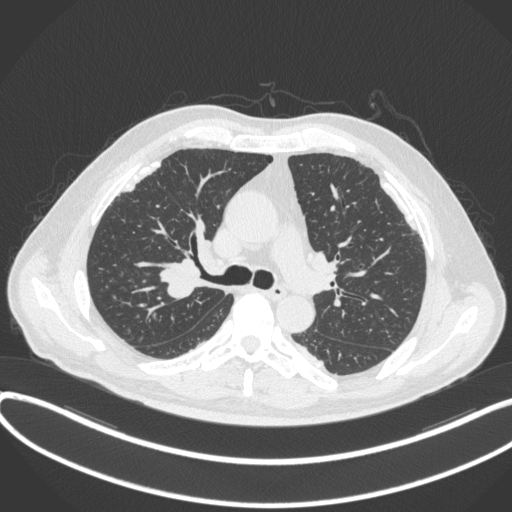
Chest CT, one axial slice; position 274 of 455 along the scan axis; reconstruction kernel B31f; lung window (W 1500 / L -600 HU); 512 × 512 image matrix. Male patient, age 58 years. From the clinical record (not read from this slice): clinical TNM (as recorded): T1c N0 M0.
Structures marked on this image (rectangle marked by the reading radiologist):
- lung tumour (recorded histology: squamous cell carcinoma): bounding box [x1, y1, x2, y2] px = [162, 256, 207, 305]